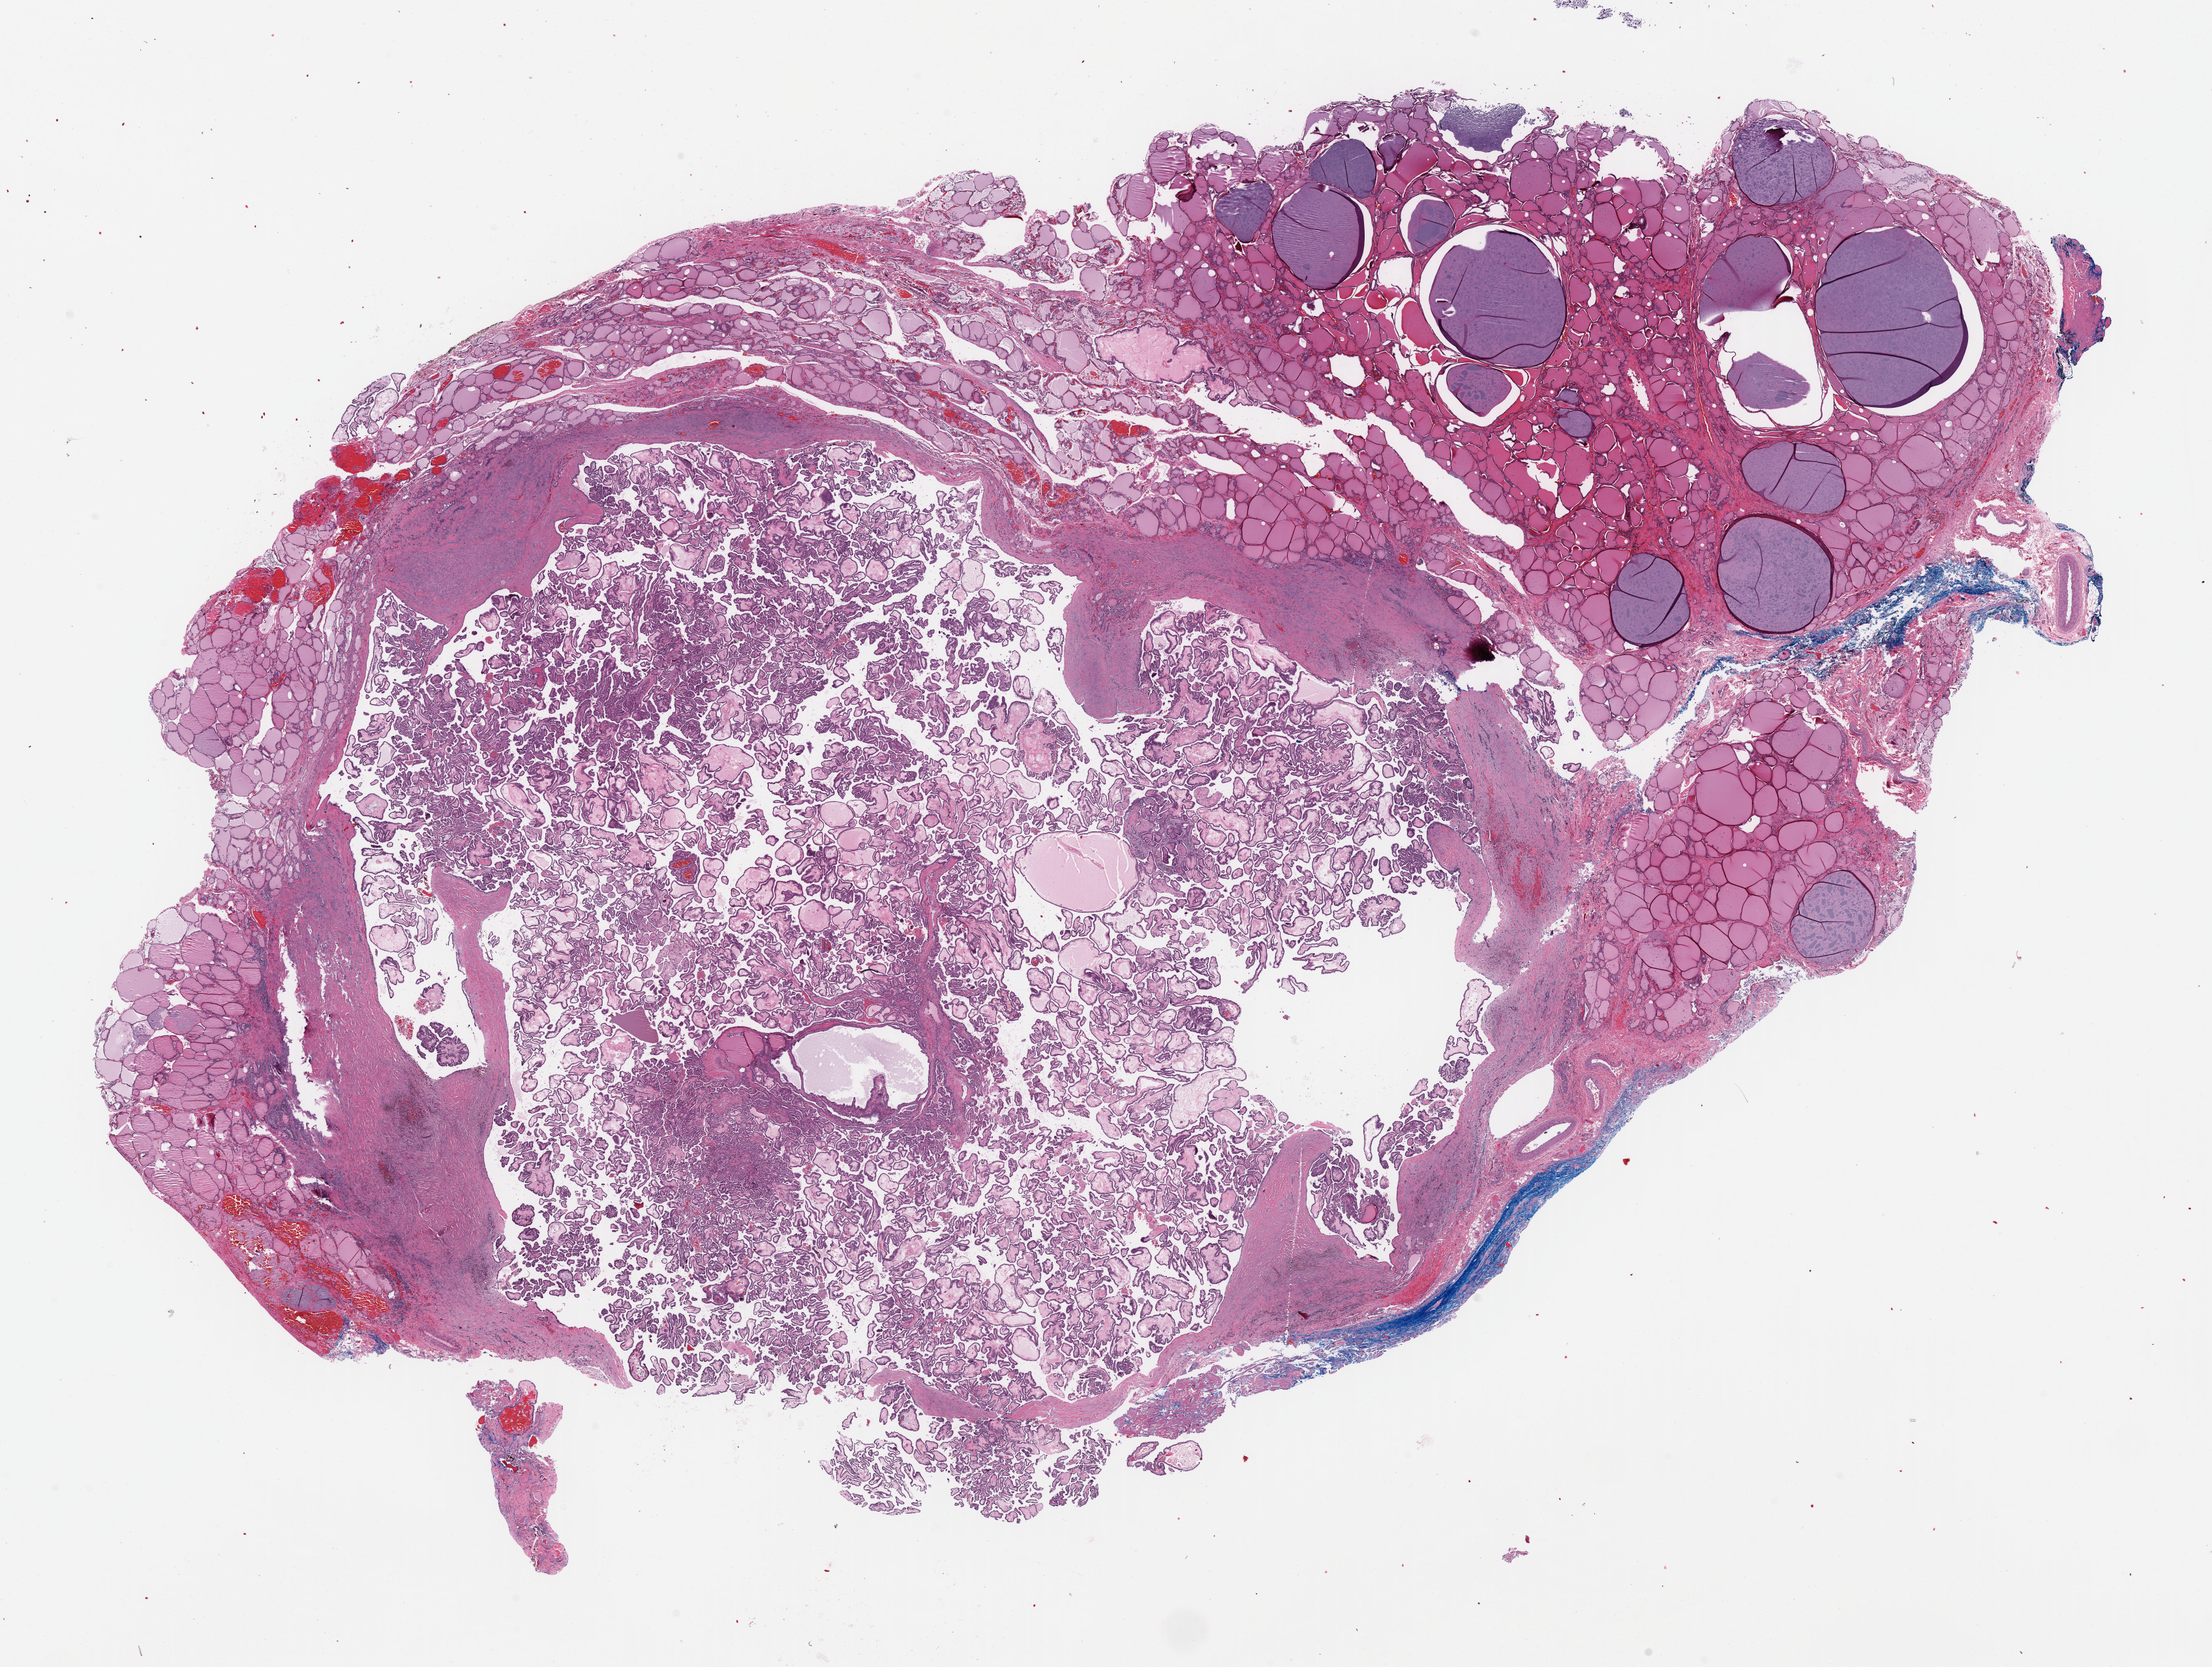
Whole-slide histology image, H&E, whole scanned area (about 26.8 x 20.2 mm, acquisition: 40x scan) shown as a low-resolution overview, formalin-fixed paraffin-embedded (FFPE) diagnostic section, thyroid, primary tumour sample. Patient: female, age at initial diagnosis 32 years.
Pathologic diagnosis: Papillary adenocarcinoma, NOS (thyroid gland). Laterality: left. AJCC pathologic stage: I (7th edition).